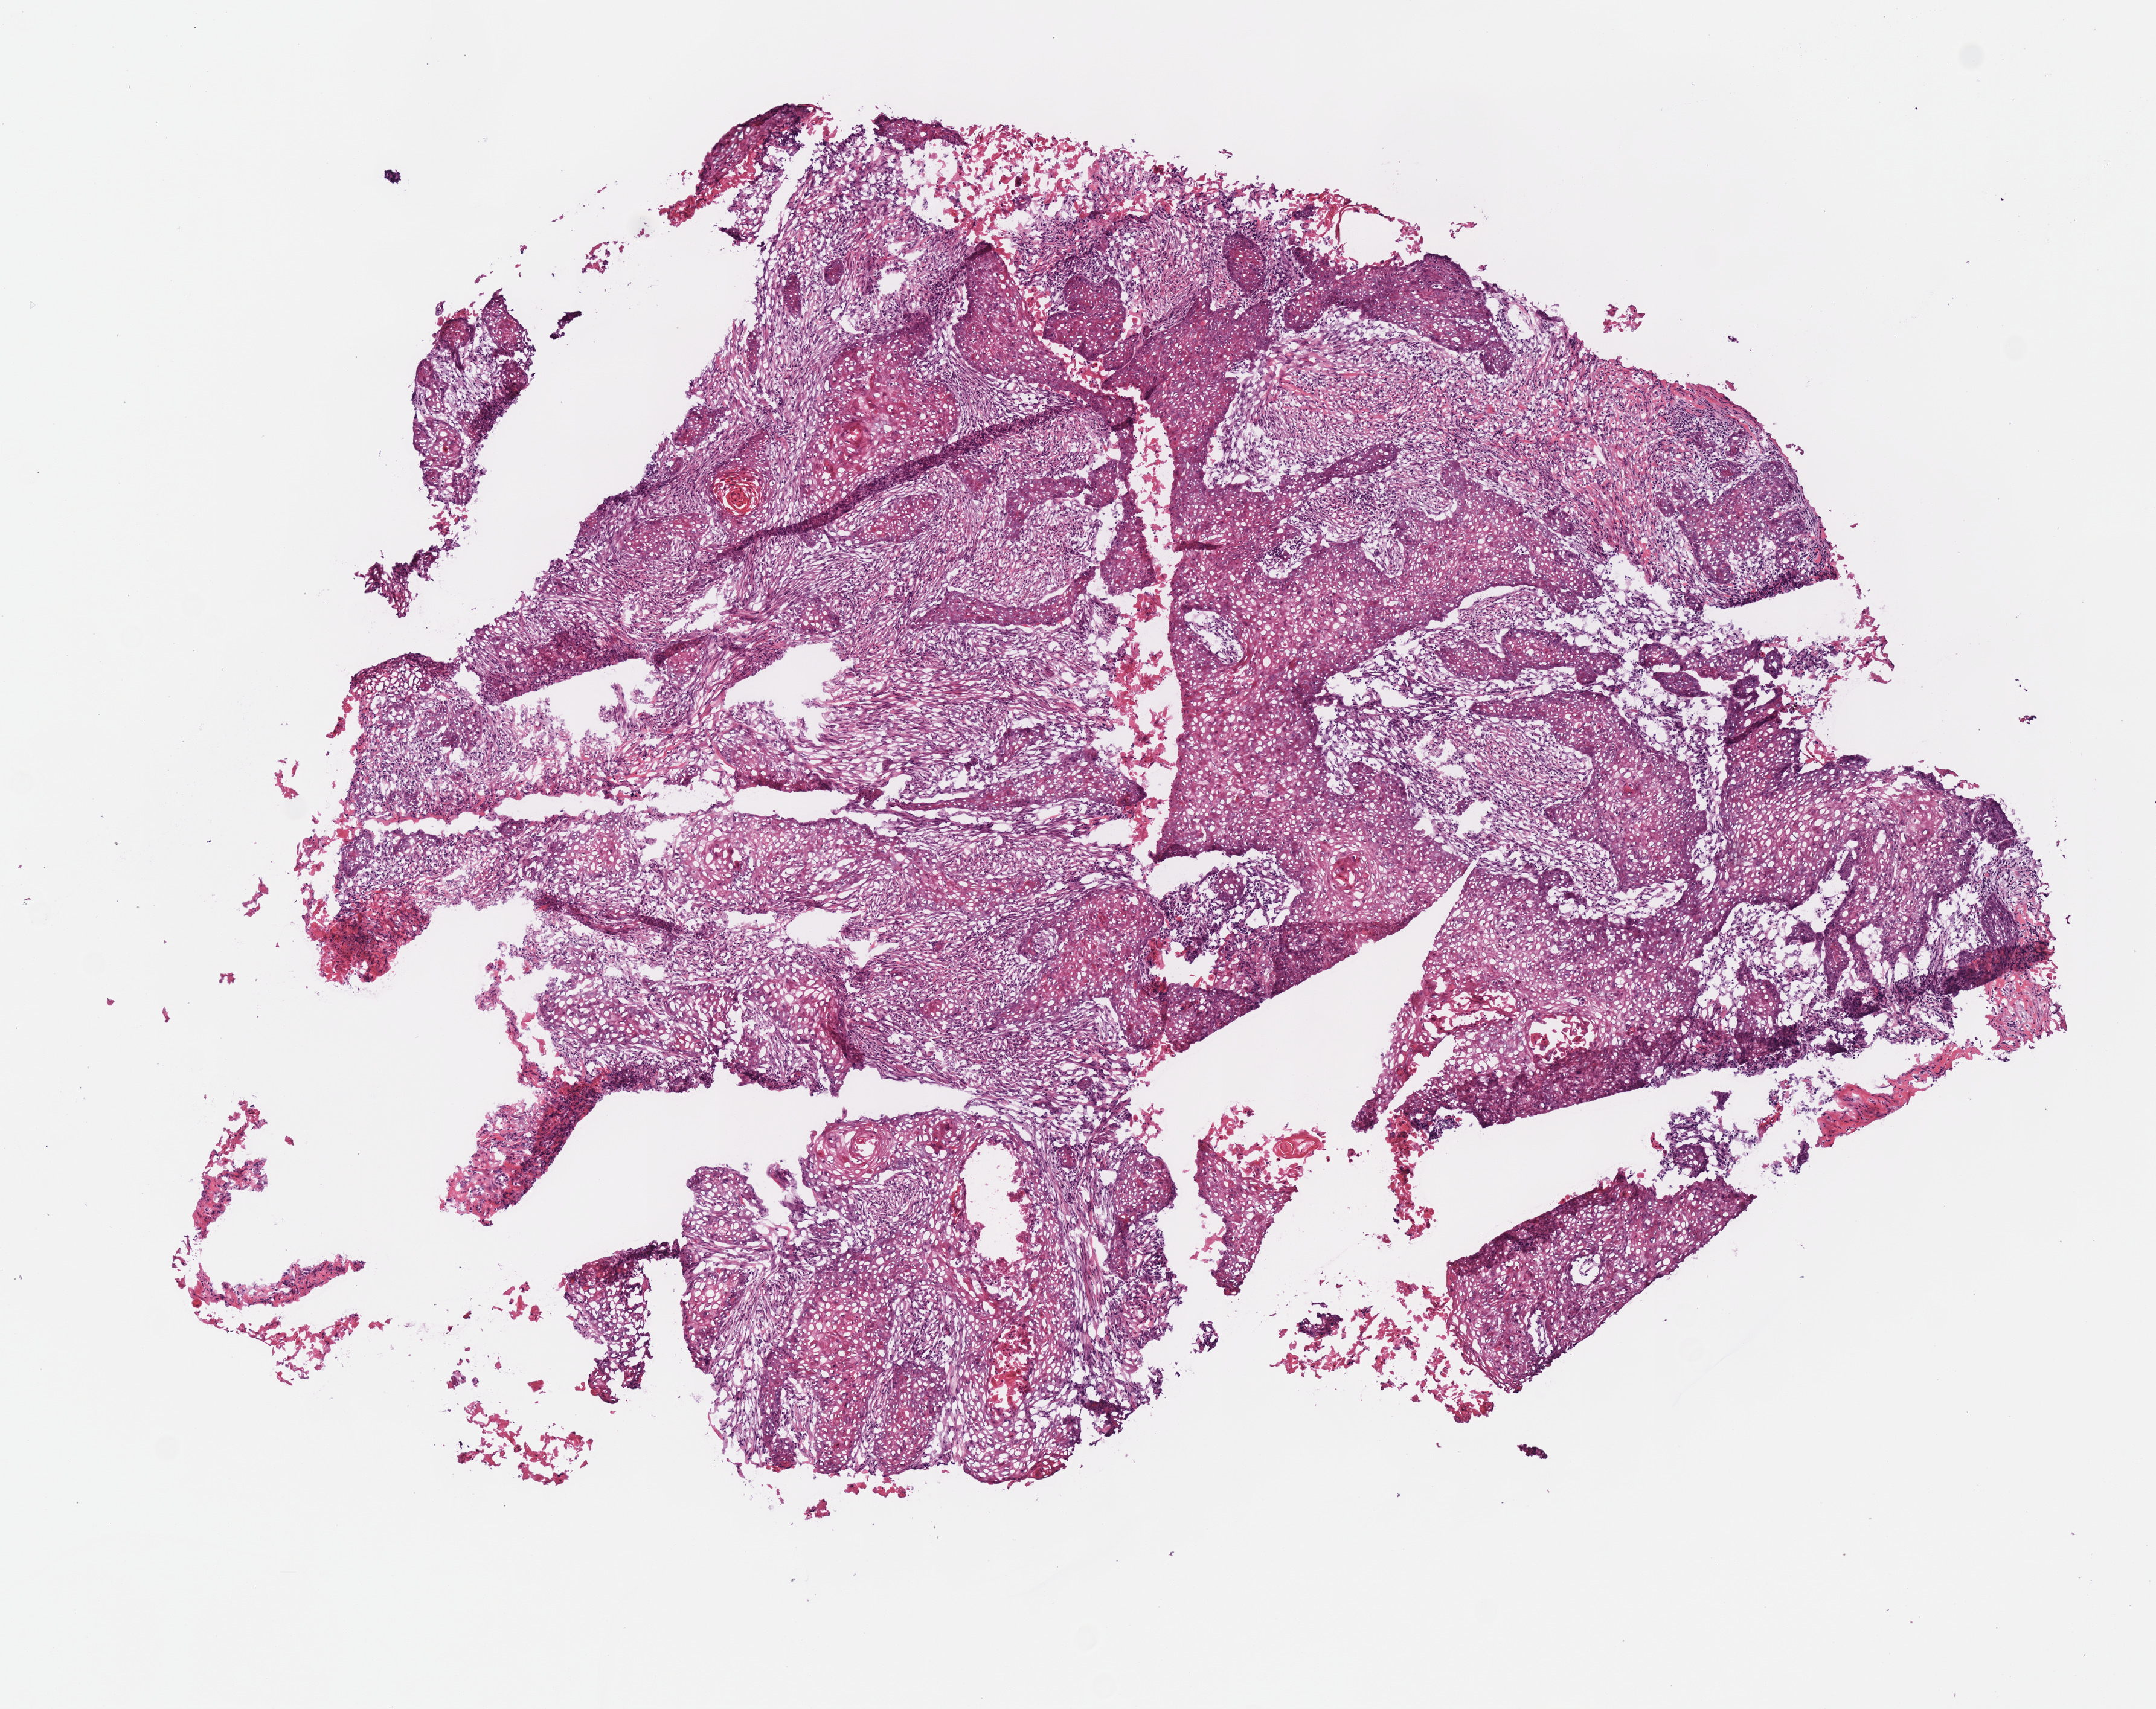
H&E whole-slide image, shown as a low-resolution overview of the whole scanned area (about 7.0 x 5.6 mm); frozen section from the bottom of the tissue portion; sample: primary tumour, head and neck. Female, age 74 years at initial diagnosis. Histologic grade: G2 (moderately differentiated). Slide review estimates, as recorded: tumour cells 92%, tumour nuclei 65%, normal cells 0%, stromal cells 8%, necrosis 0%. Infiltration values recorded for this section: lymphocyte infiltration 15%, monocyte infiltration 0%, neutrophil infiltration 0%.
Histologic diagnosis: Squamous cell carcinoma, NOS (overlapping lesion of lip, oral cavity and pharynx). AJCC pathologic stage: II (7th edition).